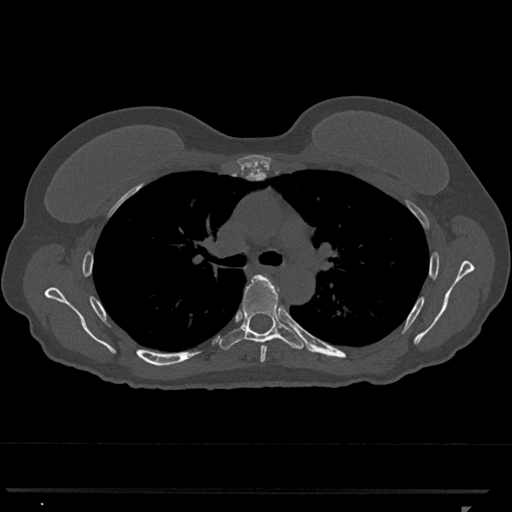
CT including the spine, one axial slice; slice 774 of 793 in the series (ordered by position); 120 kVp; bone window (W 1800 / L 400 HU); 0.5 mm slice thickness; 512 × 512 image matrix, field of view 380 × 380 mm. Female patient, age 62 years. From the clinical record (not read from this slice): primary cancer: renal.
Outlined on this slice (semi-automatic segmentation, software-assisted and operator-edited):
- T5 vertebra: box from (x=260, y=279) to (x=279, y=362) px
- T6 vertebra: (x=219, y=274)–(x=304, y=350)